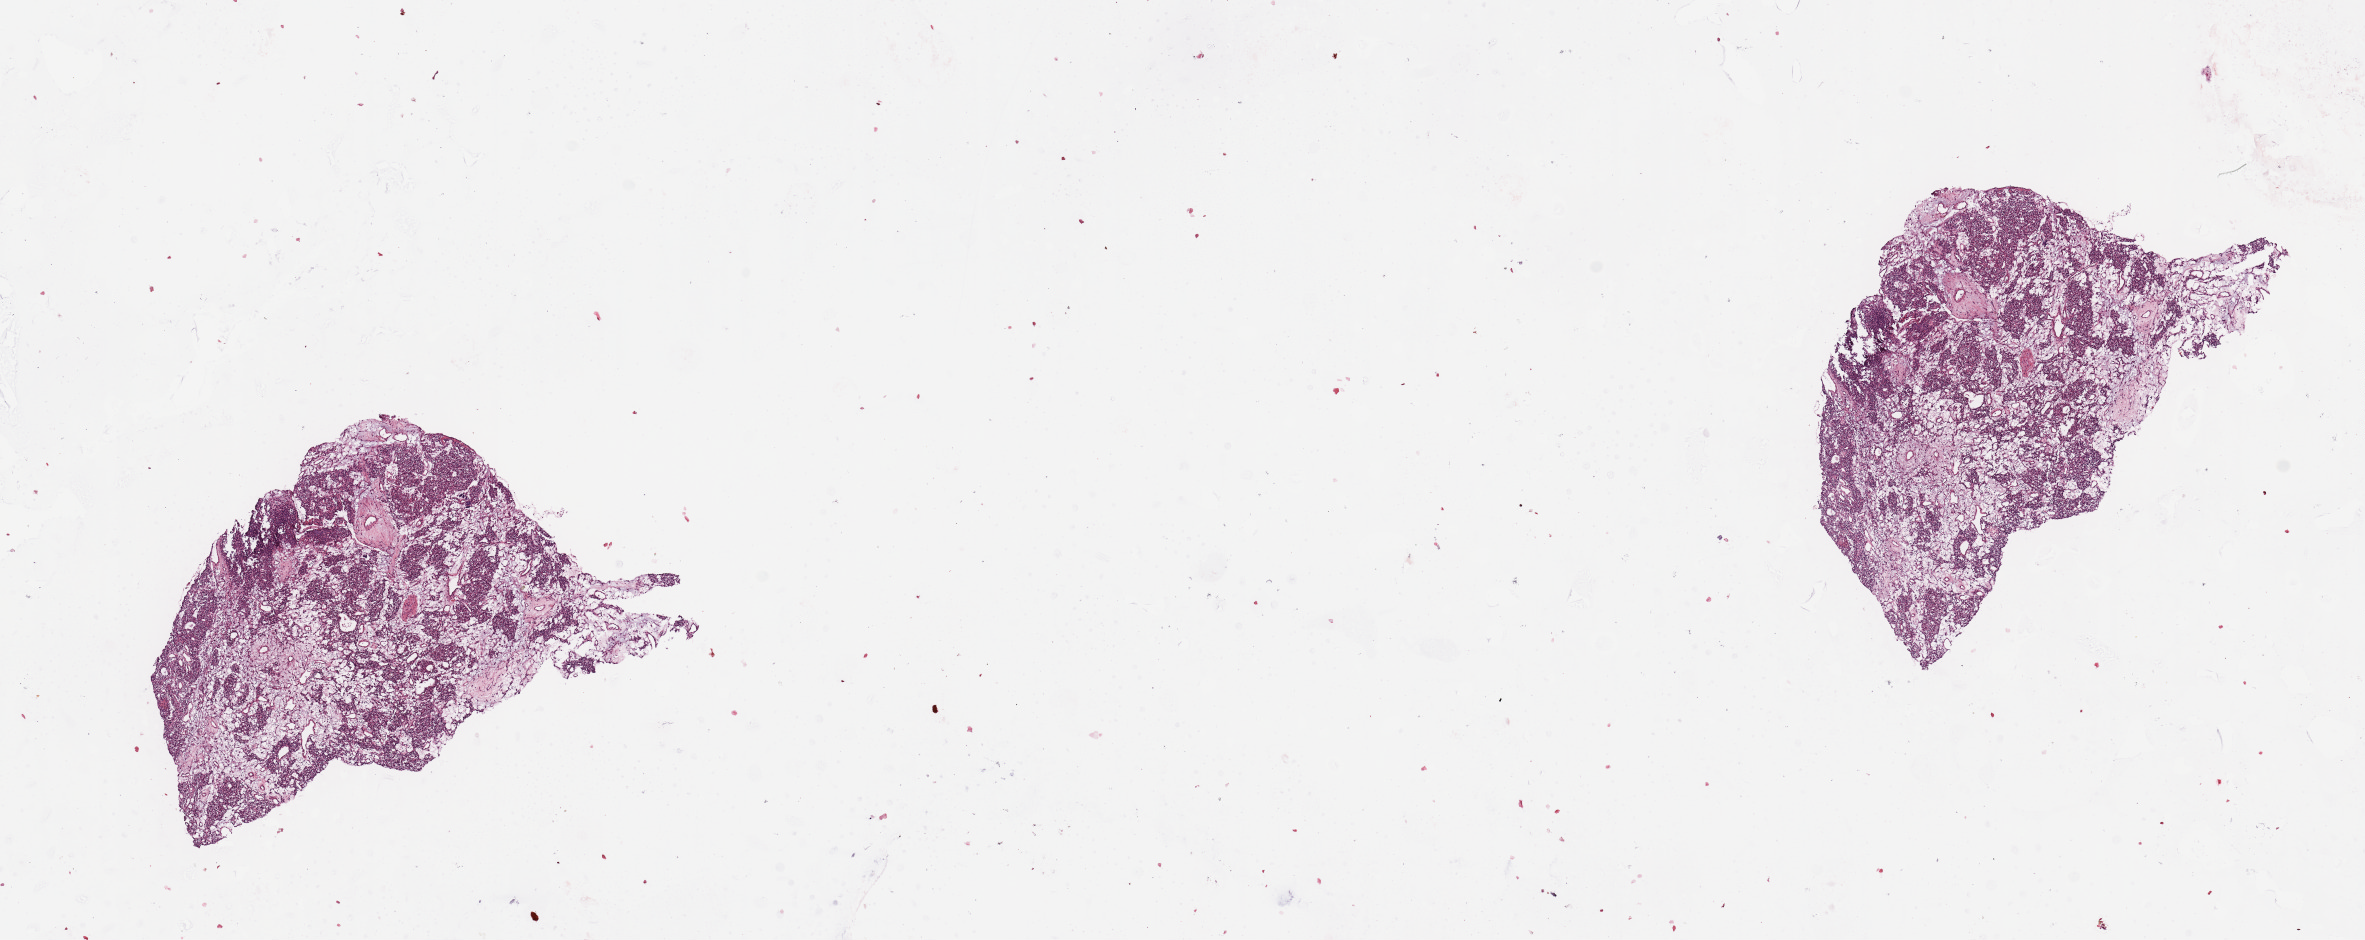
Whole-slide histology image, Hematoxylin and eosin (H&E) stained, shown as a low-resolution overview of the whole scanned area (about 18.7 x 7.4 mm, from a 20x scan); tumour tissue sample, sampled site: kidney. Patient: male, age 48 years. Histologic grade: G2 (moderately differentiated). Slide review estimates, as recorded: tumour nuclei 85%, necrosis 2%.
Histologic diagnosis: Renal cell carcinoma, NOS. Primary tumour site (as recorded): middle. AJCC pathologic stage: I.